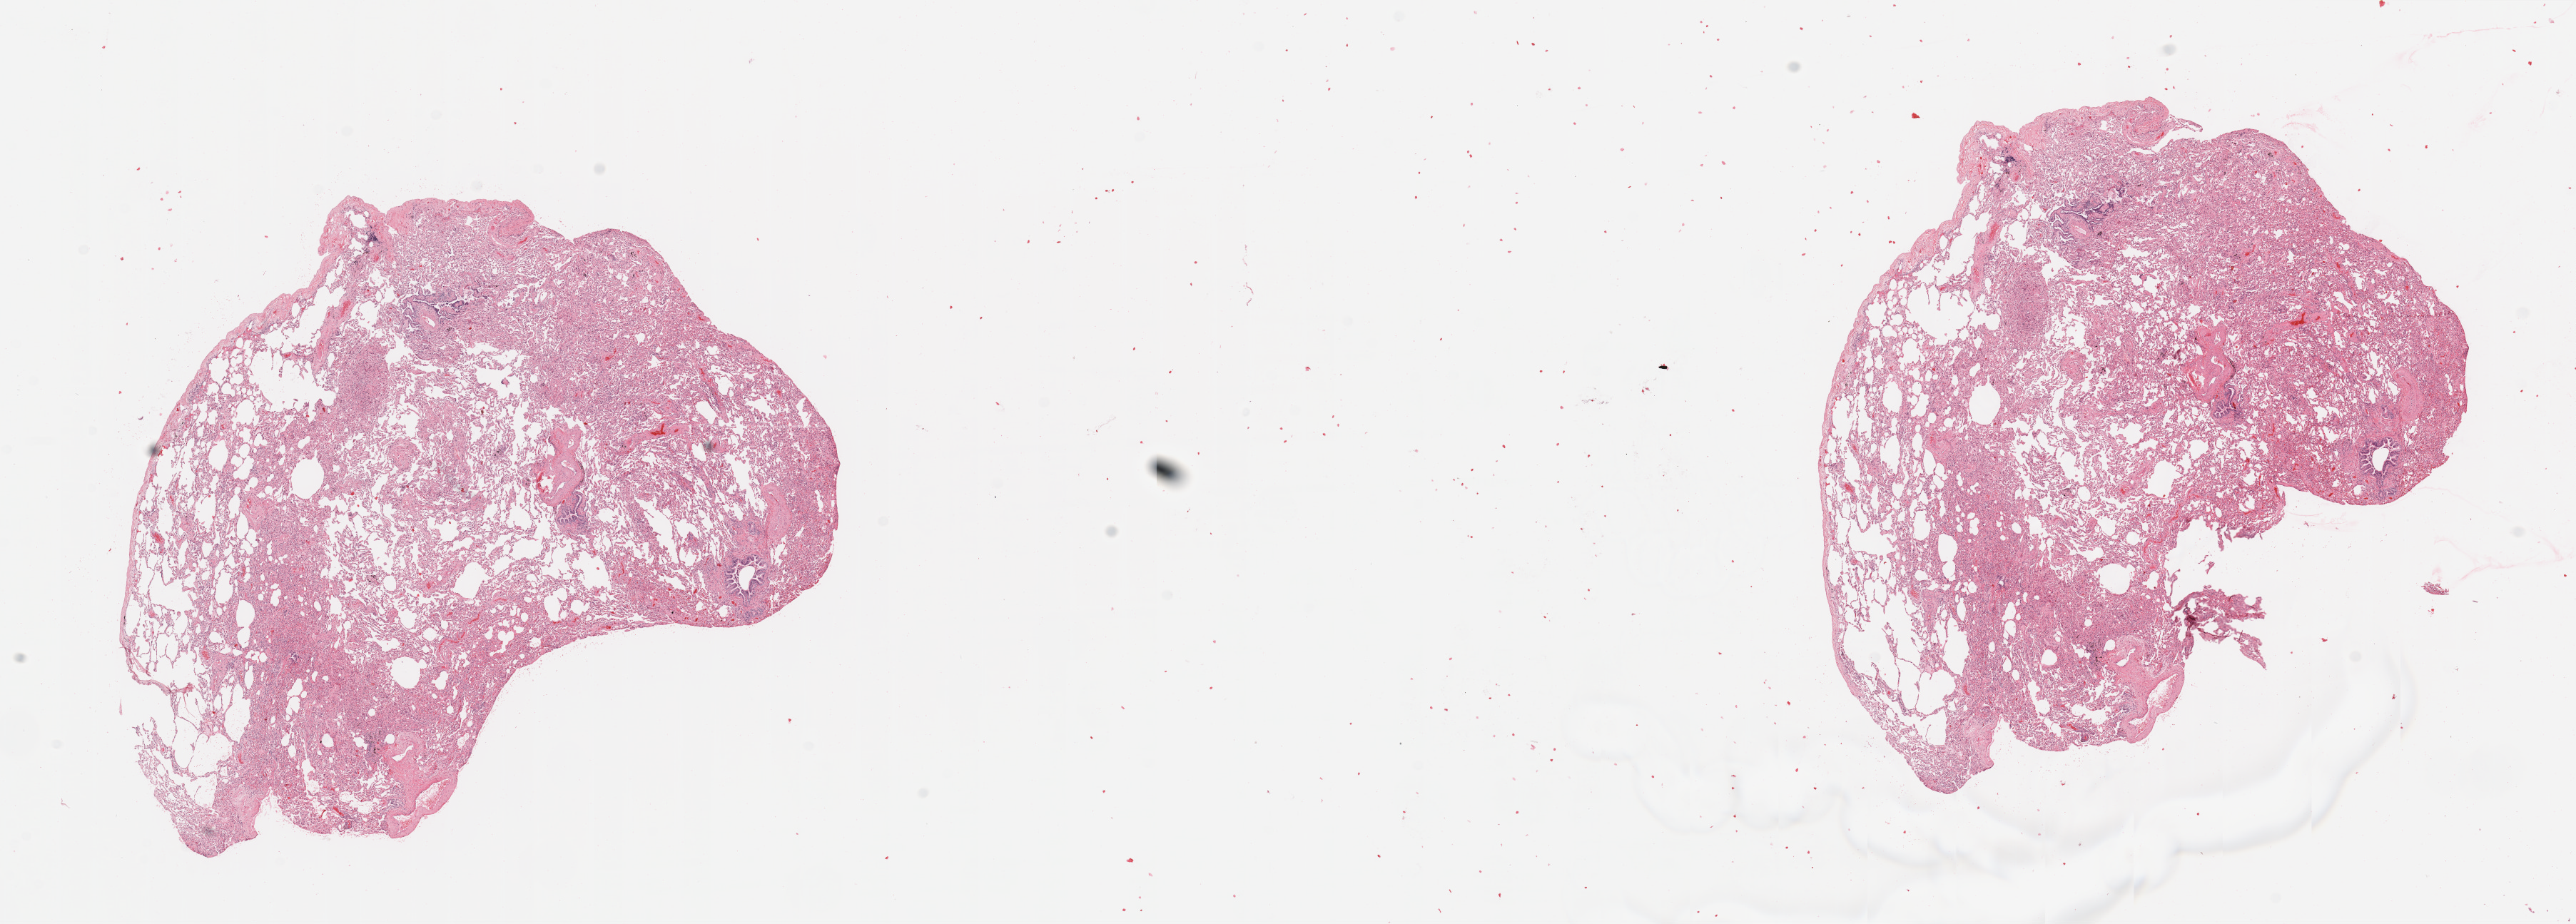
Hematoxylin and eosin (H&E) stained whole-slide image, low-resolution overview of the scanned area, about 28.5 x 10.2 mm (acquisition: 20x scan); lung, normal (non-tumour) tissue. 78-year-old male patient.
This section: normal (non-tumour) tissue from the same patient. Patient diagnosis: Adenocarcinoma, NOS.